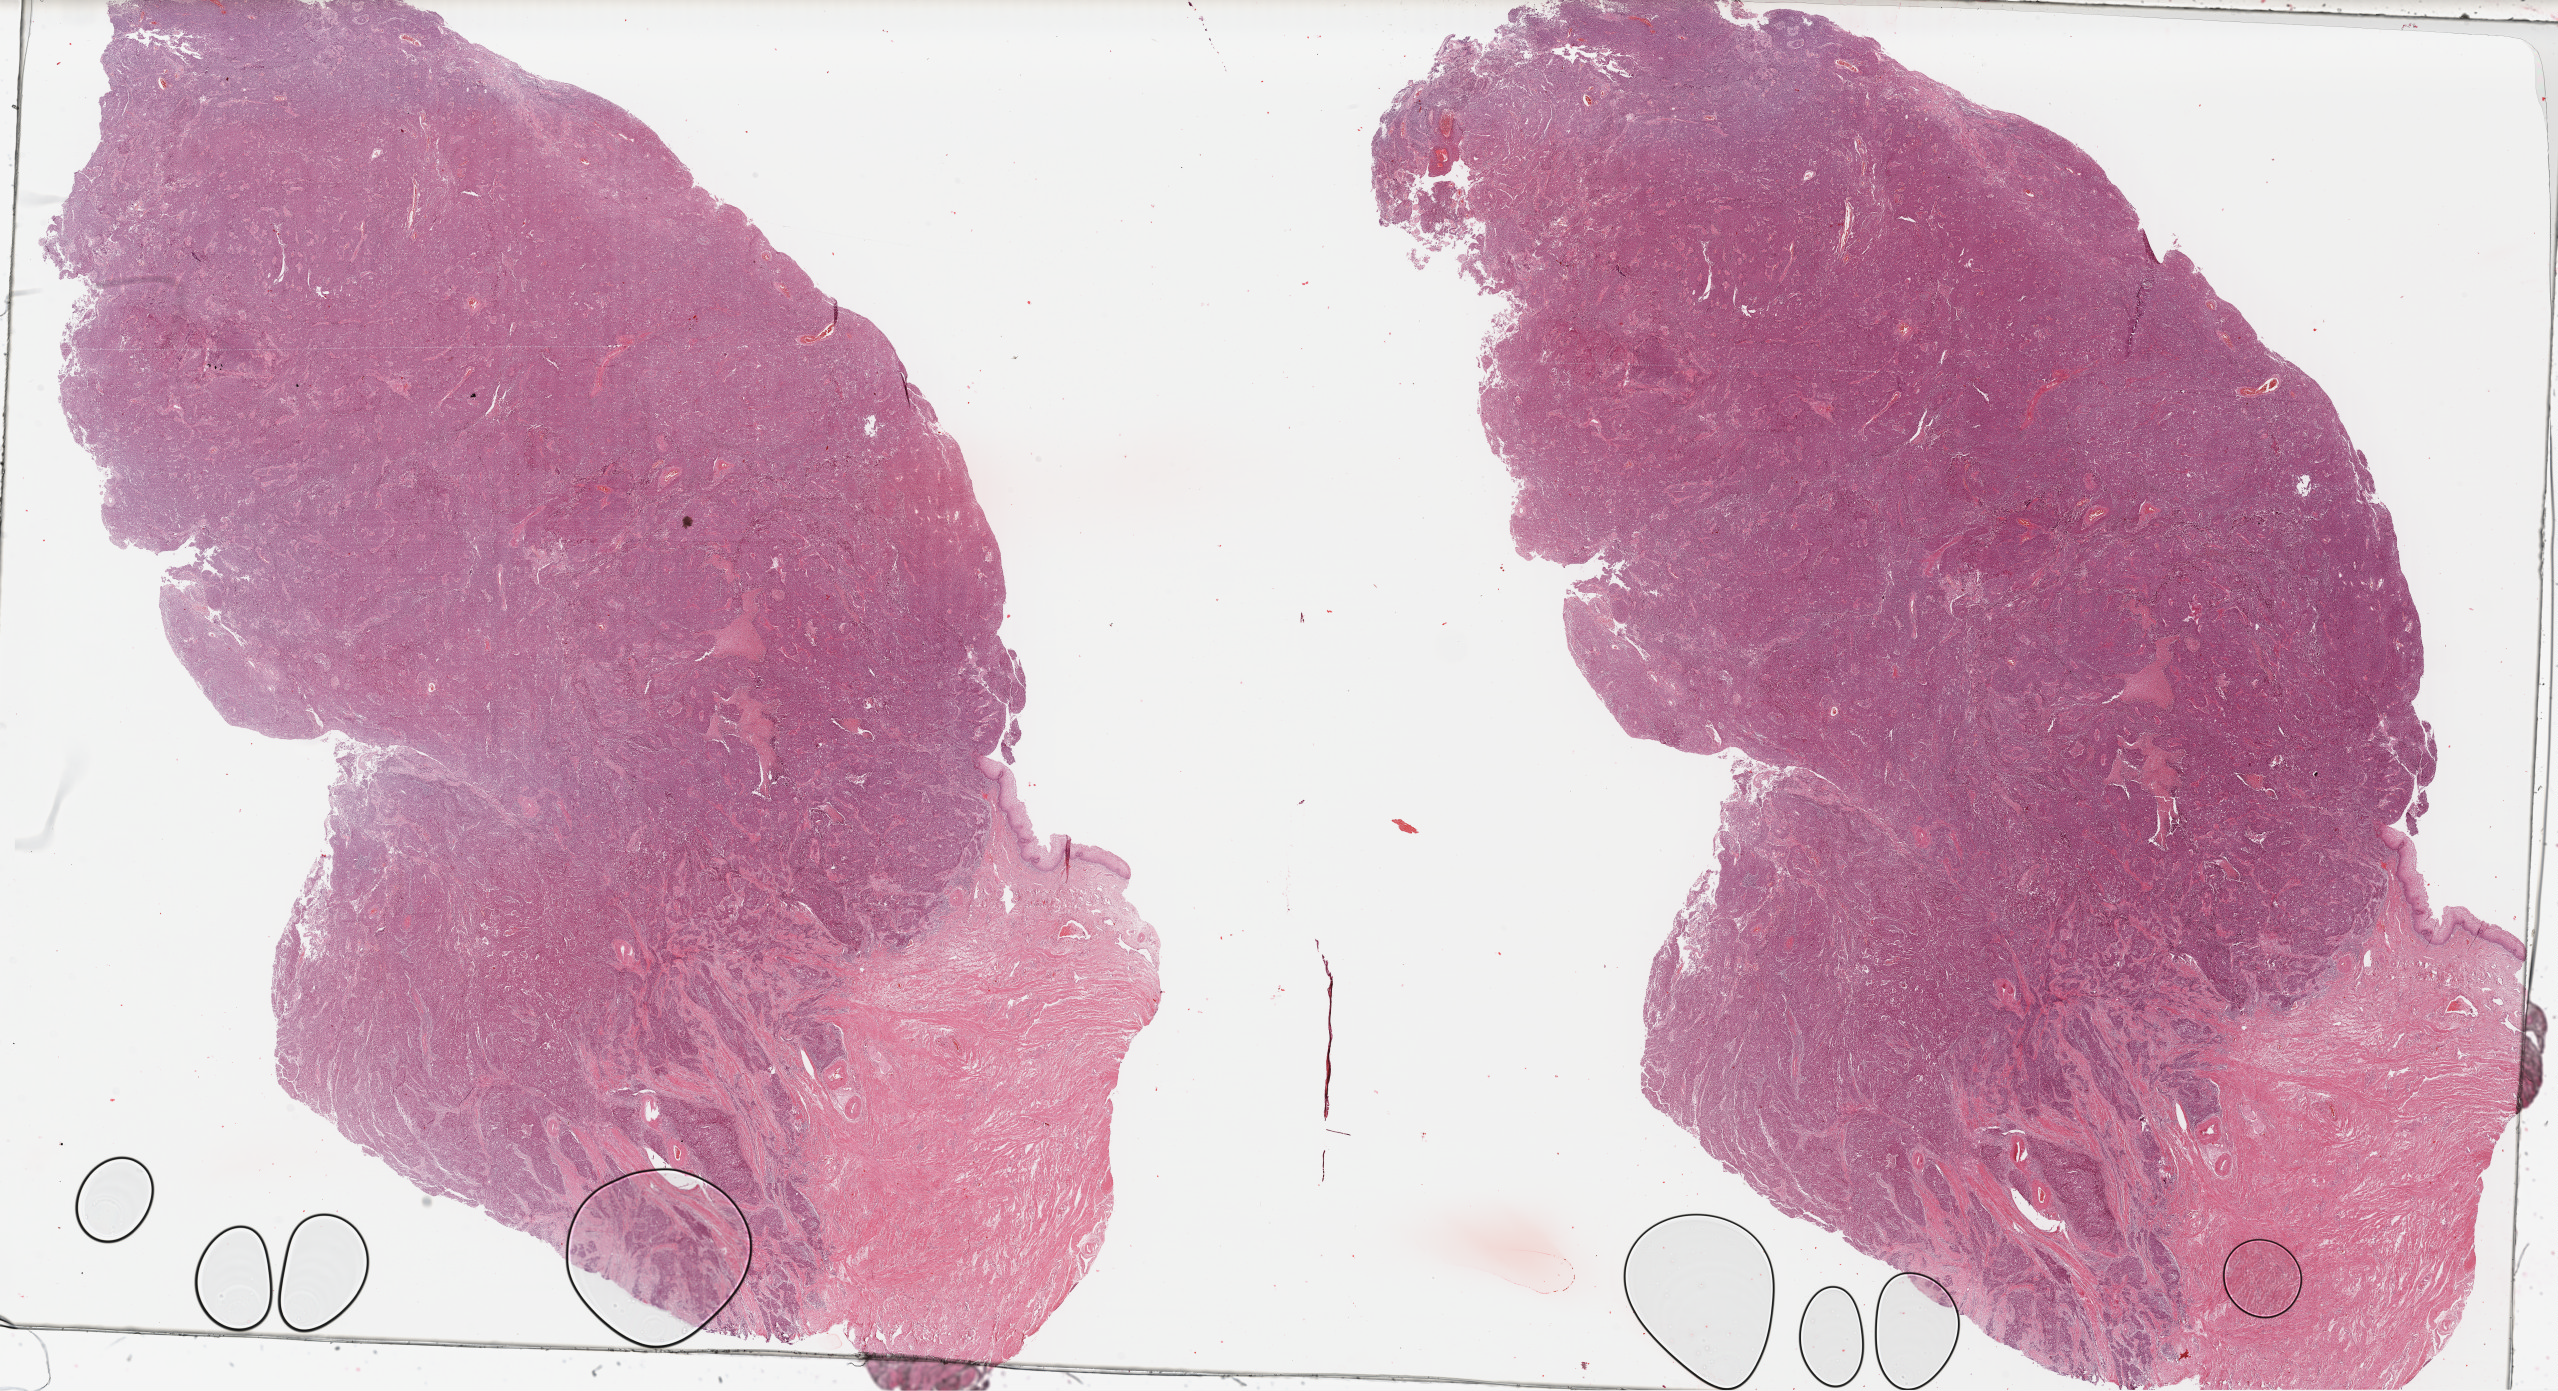
Hematoxylin and eosin (H&E) stained whole-slide image, shown as a low-resolution overview of the whole scanned area (about 40.2 x 21.9 mm, acquisition: 40x scan). Formalin-fixed paraffin-embedded (FFPE) diagnostic section. Cervix, primary tumour sample. Female, age 30 years at initial diagnosis. Histologic grade: G3 (poorly differentiated).
FIGO stage: IIIB. Histologic diagnosis: Adenocarcinoma, endocervical type (cervix uteri).